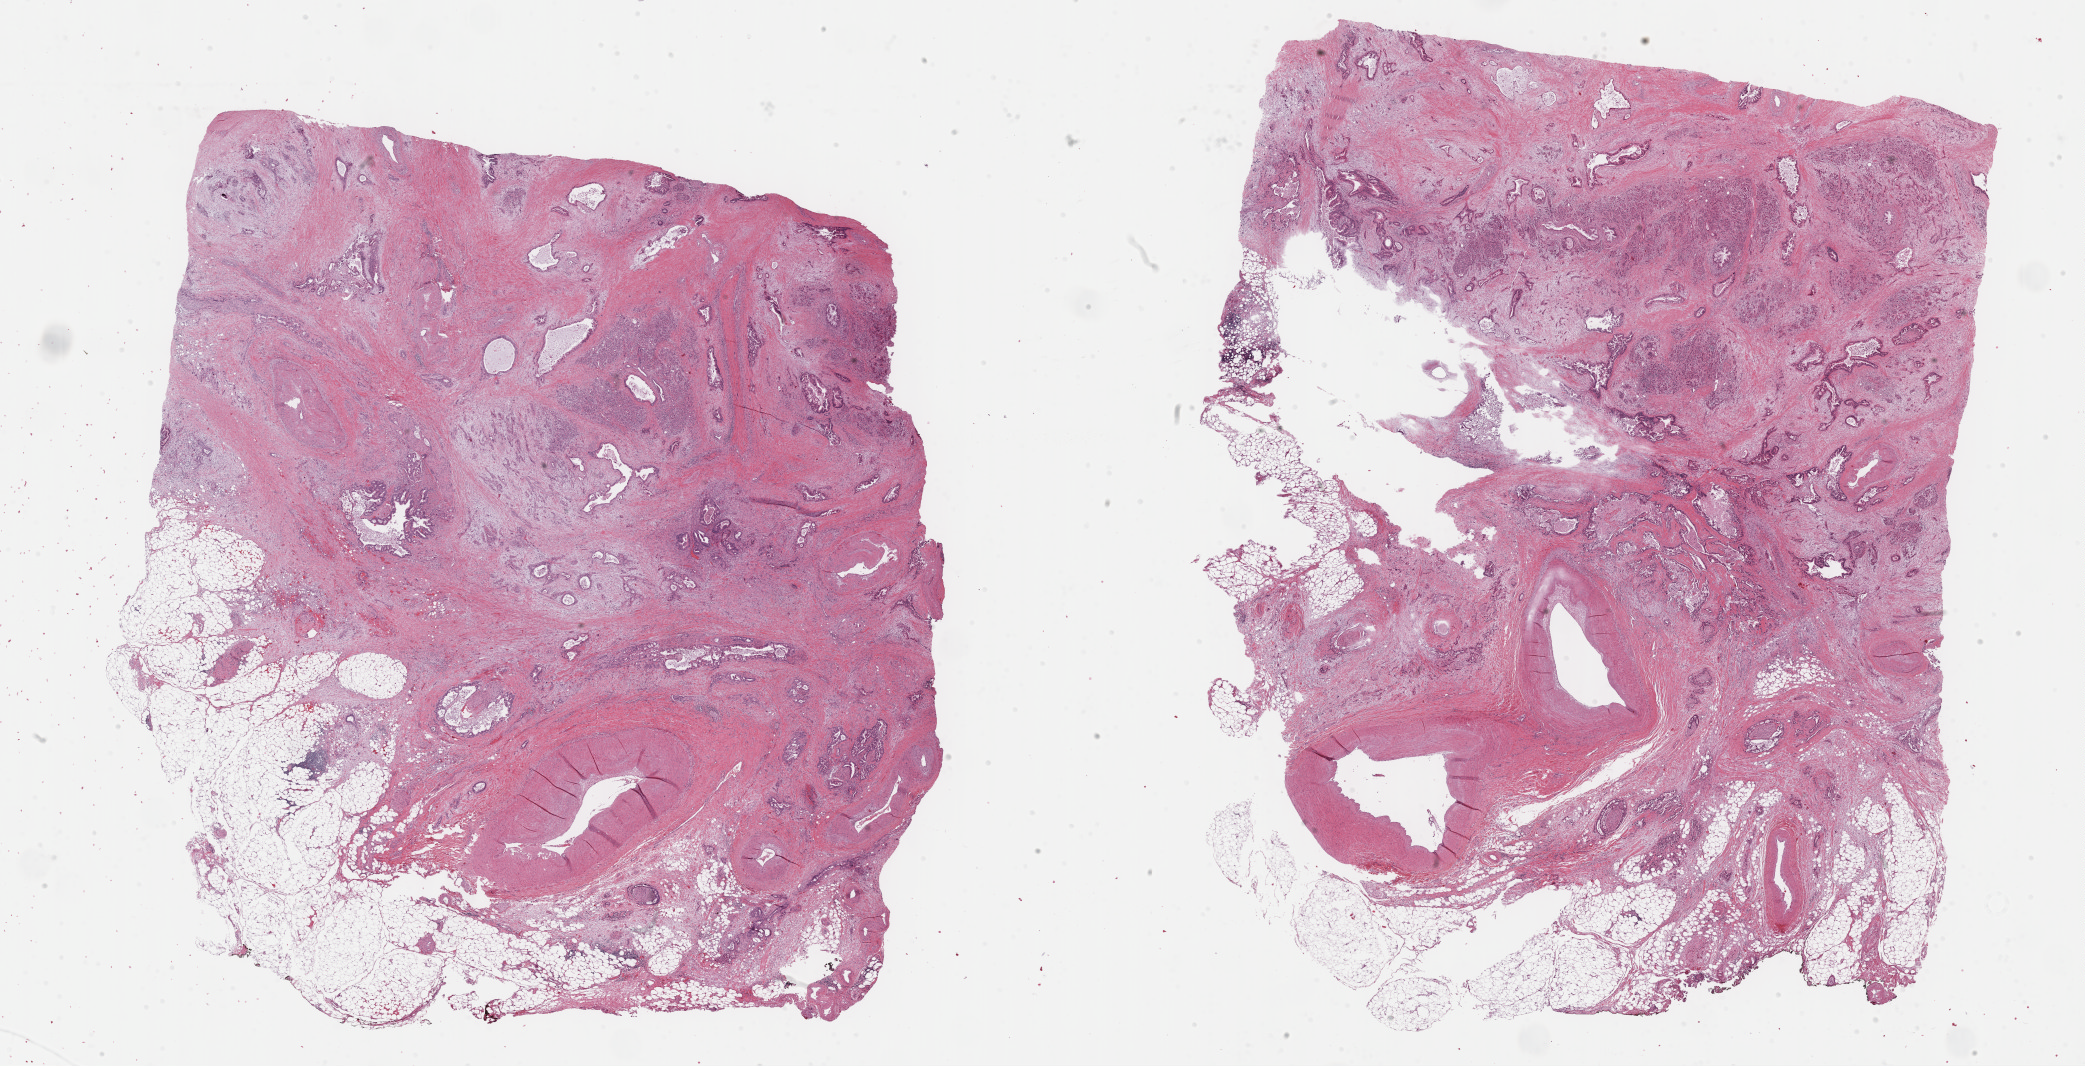
Hematoxylin and eosin (H&E) stained whole-slide image, whole scanned area (about 33.7 x 17.2 mm) shown as a low-resolution overview, formalin-fixed paraffin-embedded (FFPE) diagnostic section, primary tumour sample from the pancreas. Patient: female, age at initial diagnosis 70 years. Histologic grade: G1 (well differentiated).
TNM: T3 N1 M0. AJCC pathologic stage: IIB. Diagnosis: Infiltrating duct carcinoma, NOS.